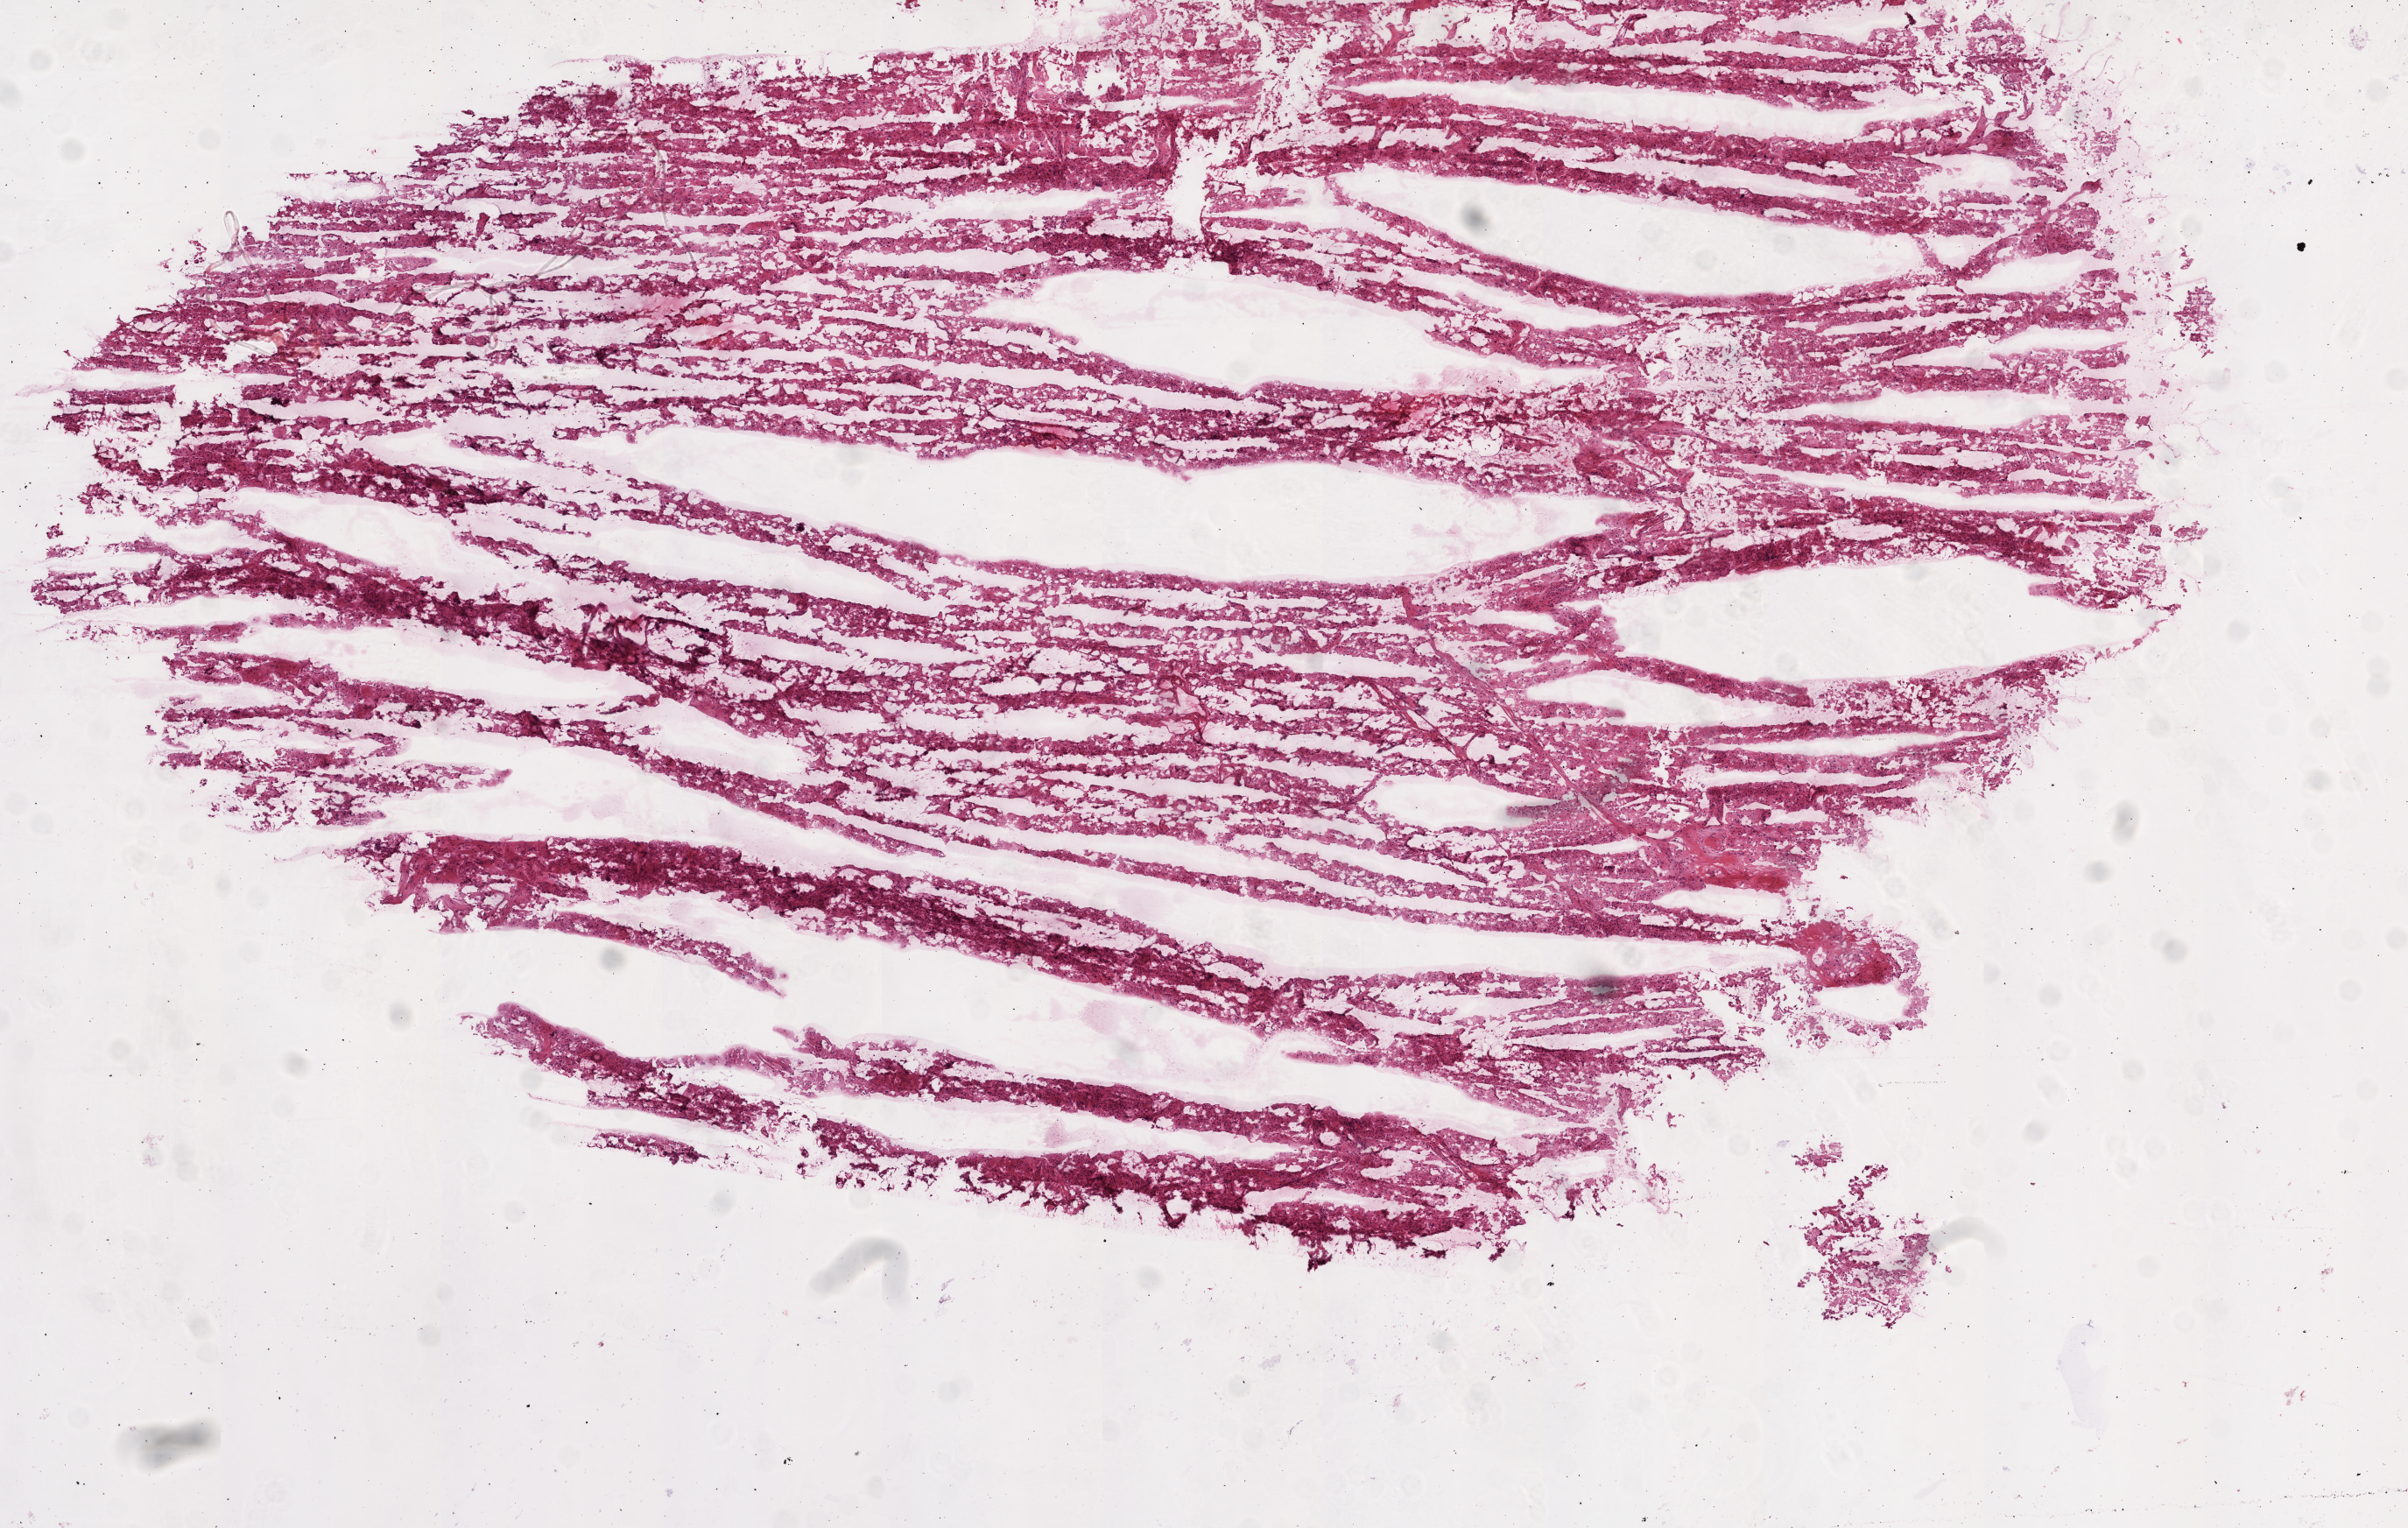
Hematoxylin and eosin (H&E) stained whole-slide image, shown as a low-resolution overview of the whole scanned area (about 11.0 x 7.0 mm, slide scanned at 20x); frozen section; kidney, primary tumour sample. Male patient; age at initial diagnosis 40 years. Histologic grade: G2 (moderately differentiated). Slide review estimates, as recorded: tumour cells 90%, tumour nuclei 85%, normal cells 0%, stromal cells 10%, necrosis 0%.
* TNM: T1b NX M0
* AJCC pathologic stage: I (7th edition)
* histologic diagnosis: Clear cell adenocarcinoma, NOS
* laterality: right